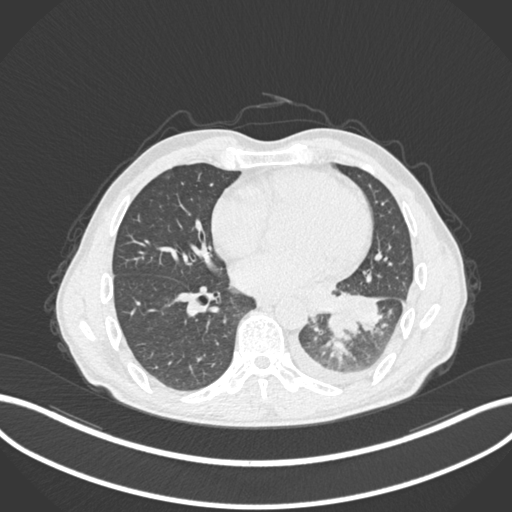
Chest CT, one axial slice; reconstruction kernel B30f; 120 kVp; lung window (W 1500 / L -600 HU); 512 × 512 image matrix, field of view 400 × 400 mm. Male patient, age 47 years. From the clinical record (not read from this slice): clinical TNM (as recorded): T3 N1 M1c; histopathological grade: G3.
Structures marked on this image (bounding box drawn by a radiologist):
- lung tumour (recorded histology: small cell carcinoma): bounding box (x1, y1, x2, y2) in pixels: (326, 311, 359, 342)